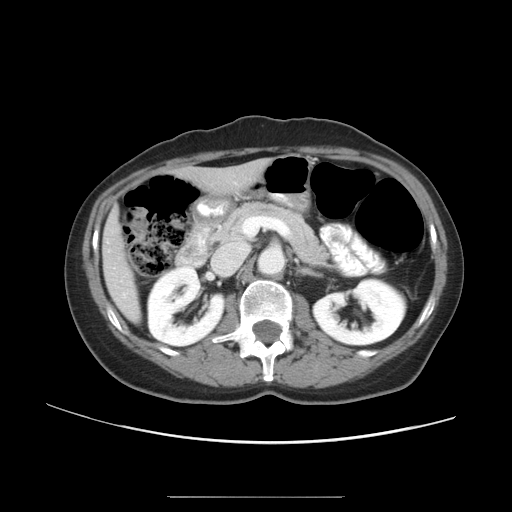
Contrast-enhanced abdominal CT, one axial slice. Position 23 of 50 along the scan axis. 120 kVp. Intravenous contrast given. Soft-tissue window (W 400 / L 40 HU). 5 mm slice thickness. 512 × 512 image matrix, field of view 389 × 389 mm. Female patient, age 58 years. From the clinical record (not read from this slice): diagnosis: colorectal cancer liver metastases, imaged before liver resection; multiple liver metastases: yes; largest metastasis: 7.3 cm; chemotherapy before resection: yes.
Structures marked on this image (manually delineated by an expert):
- liver: bounding box <105,164,262,319> (left, top, right, bottom; pixels)
- planned liver remnant (the part of the liver to remain after resection): <198,164,262,190>